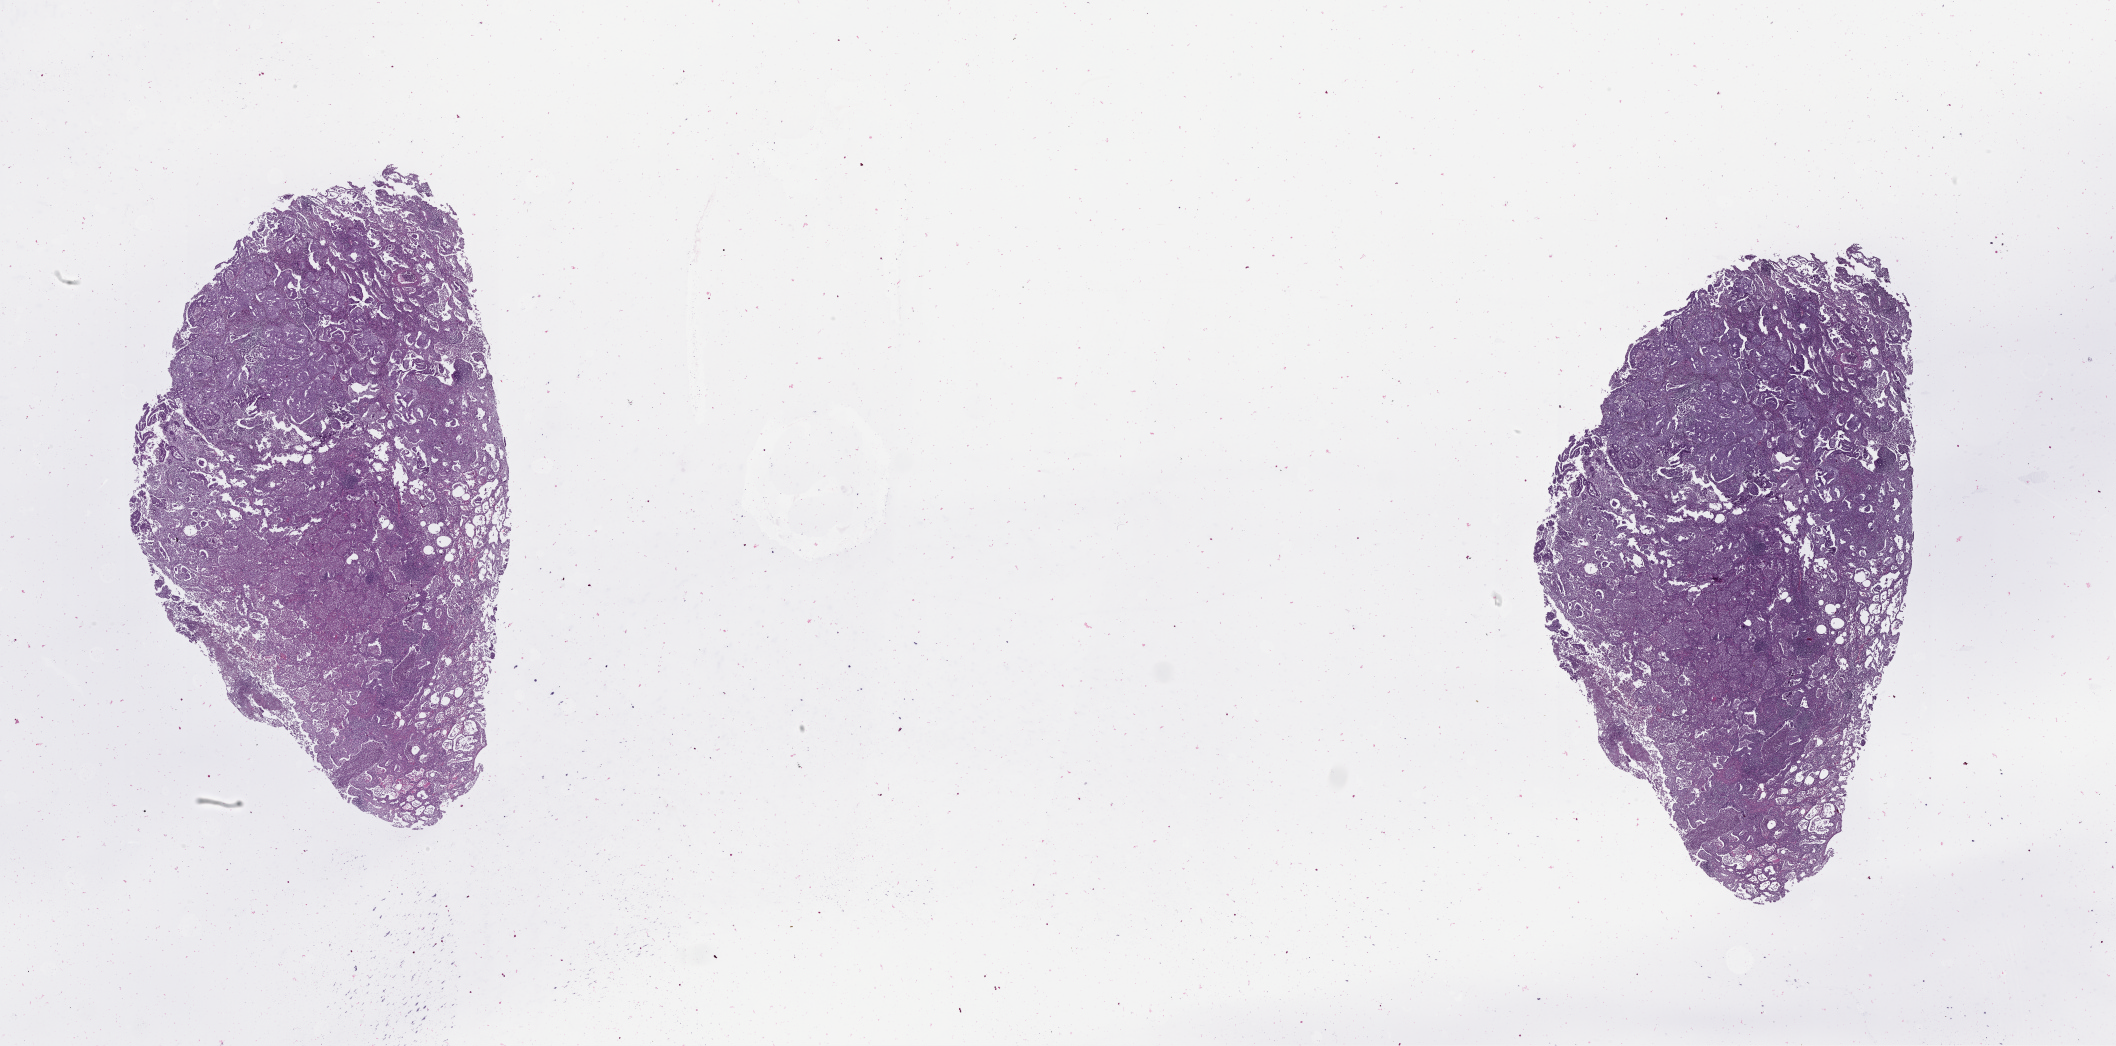
Digitized Hematoxylin and eosin (H&E) stained tissue section (whole slide) — low-resolution overview of the scanned area, about 34.1 x 16.8 mm (acquisition: 20x scan); lung, tissue type not recorded.
Patient diagnosis (cohort enrolment): lung adenocarcinoma (lung).